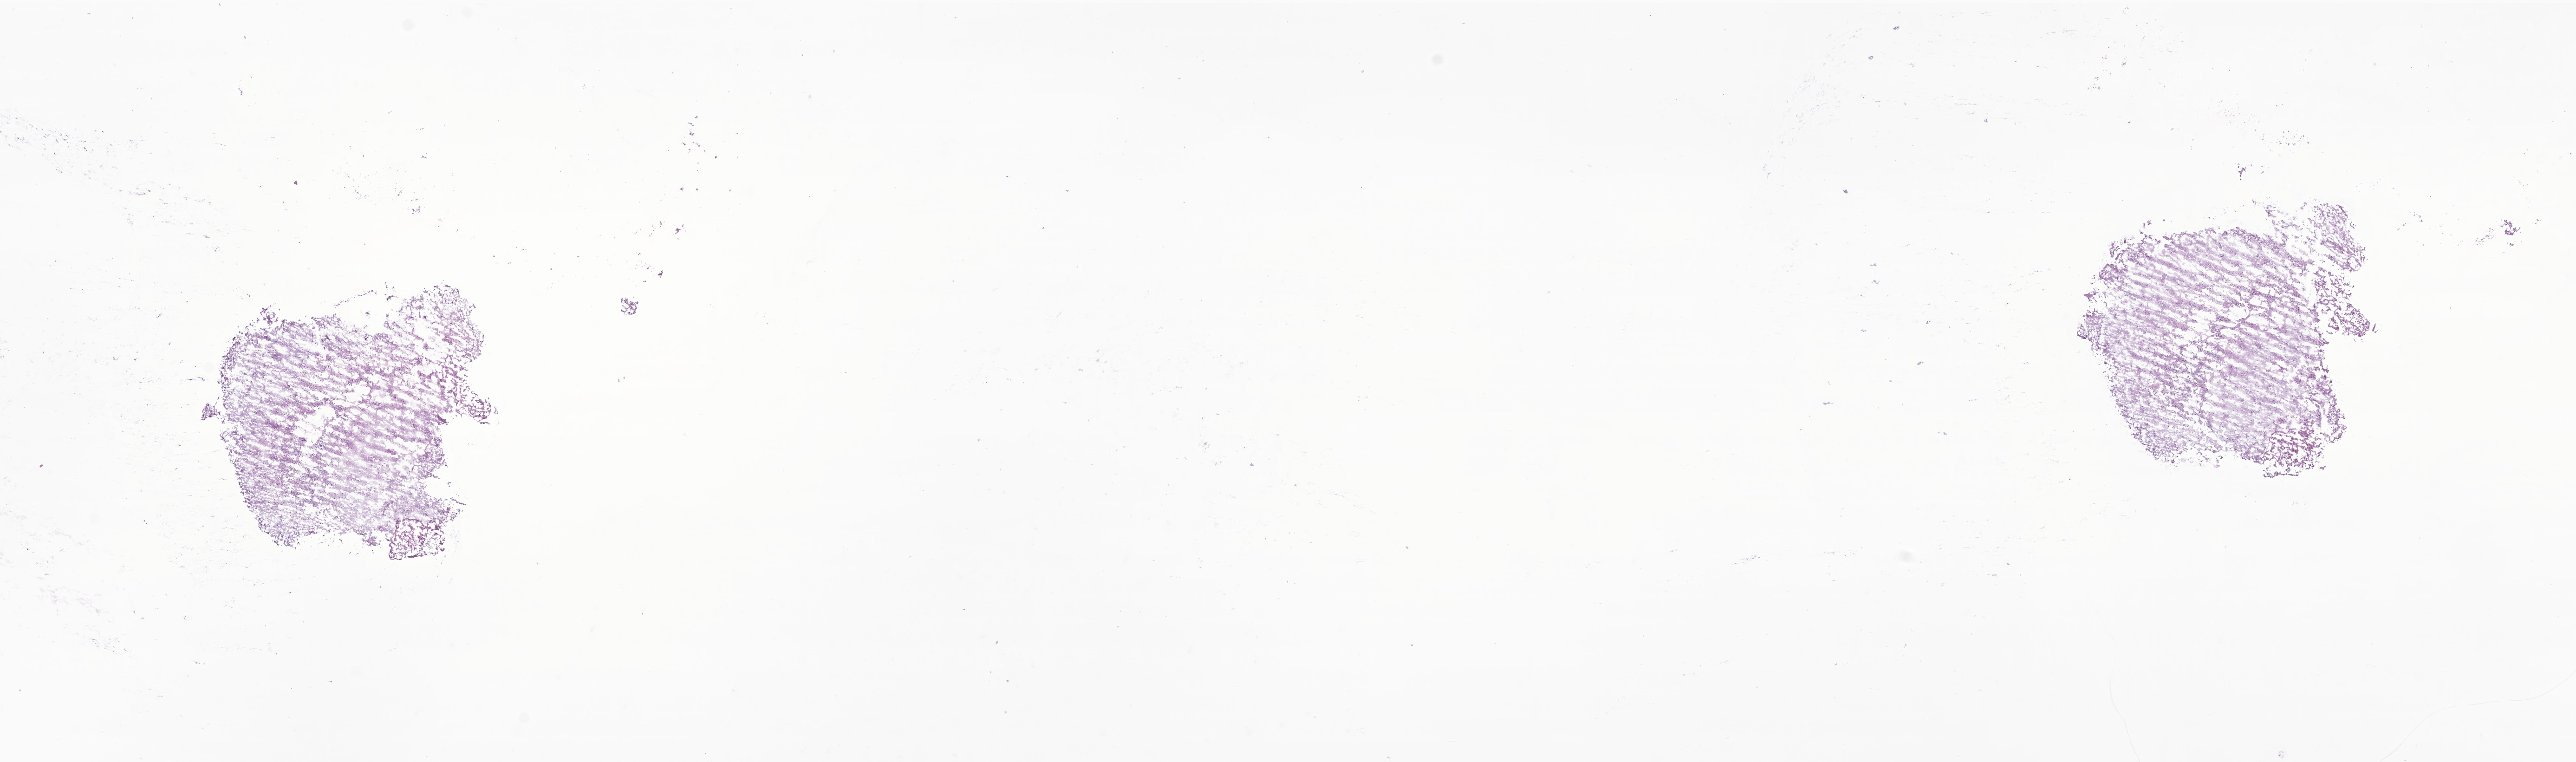
Hematoxylin and eosin (H&E) whole-slide image of tumor tissue from the brain — low-resolution overview of the scanned area, about 23.4 x 6.9 mm; frozen section (OCT-embedded). Patient: male, age 82 months (6 years 10 months).
Recorded diagnosis: Neoplasm, malignant.